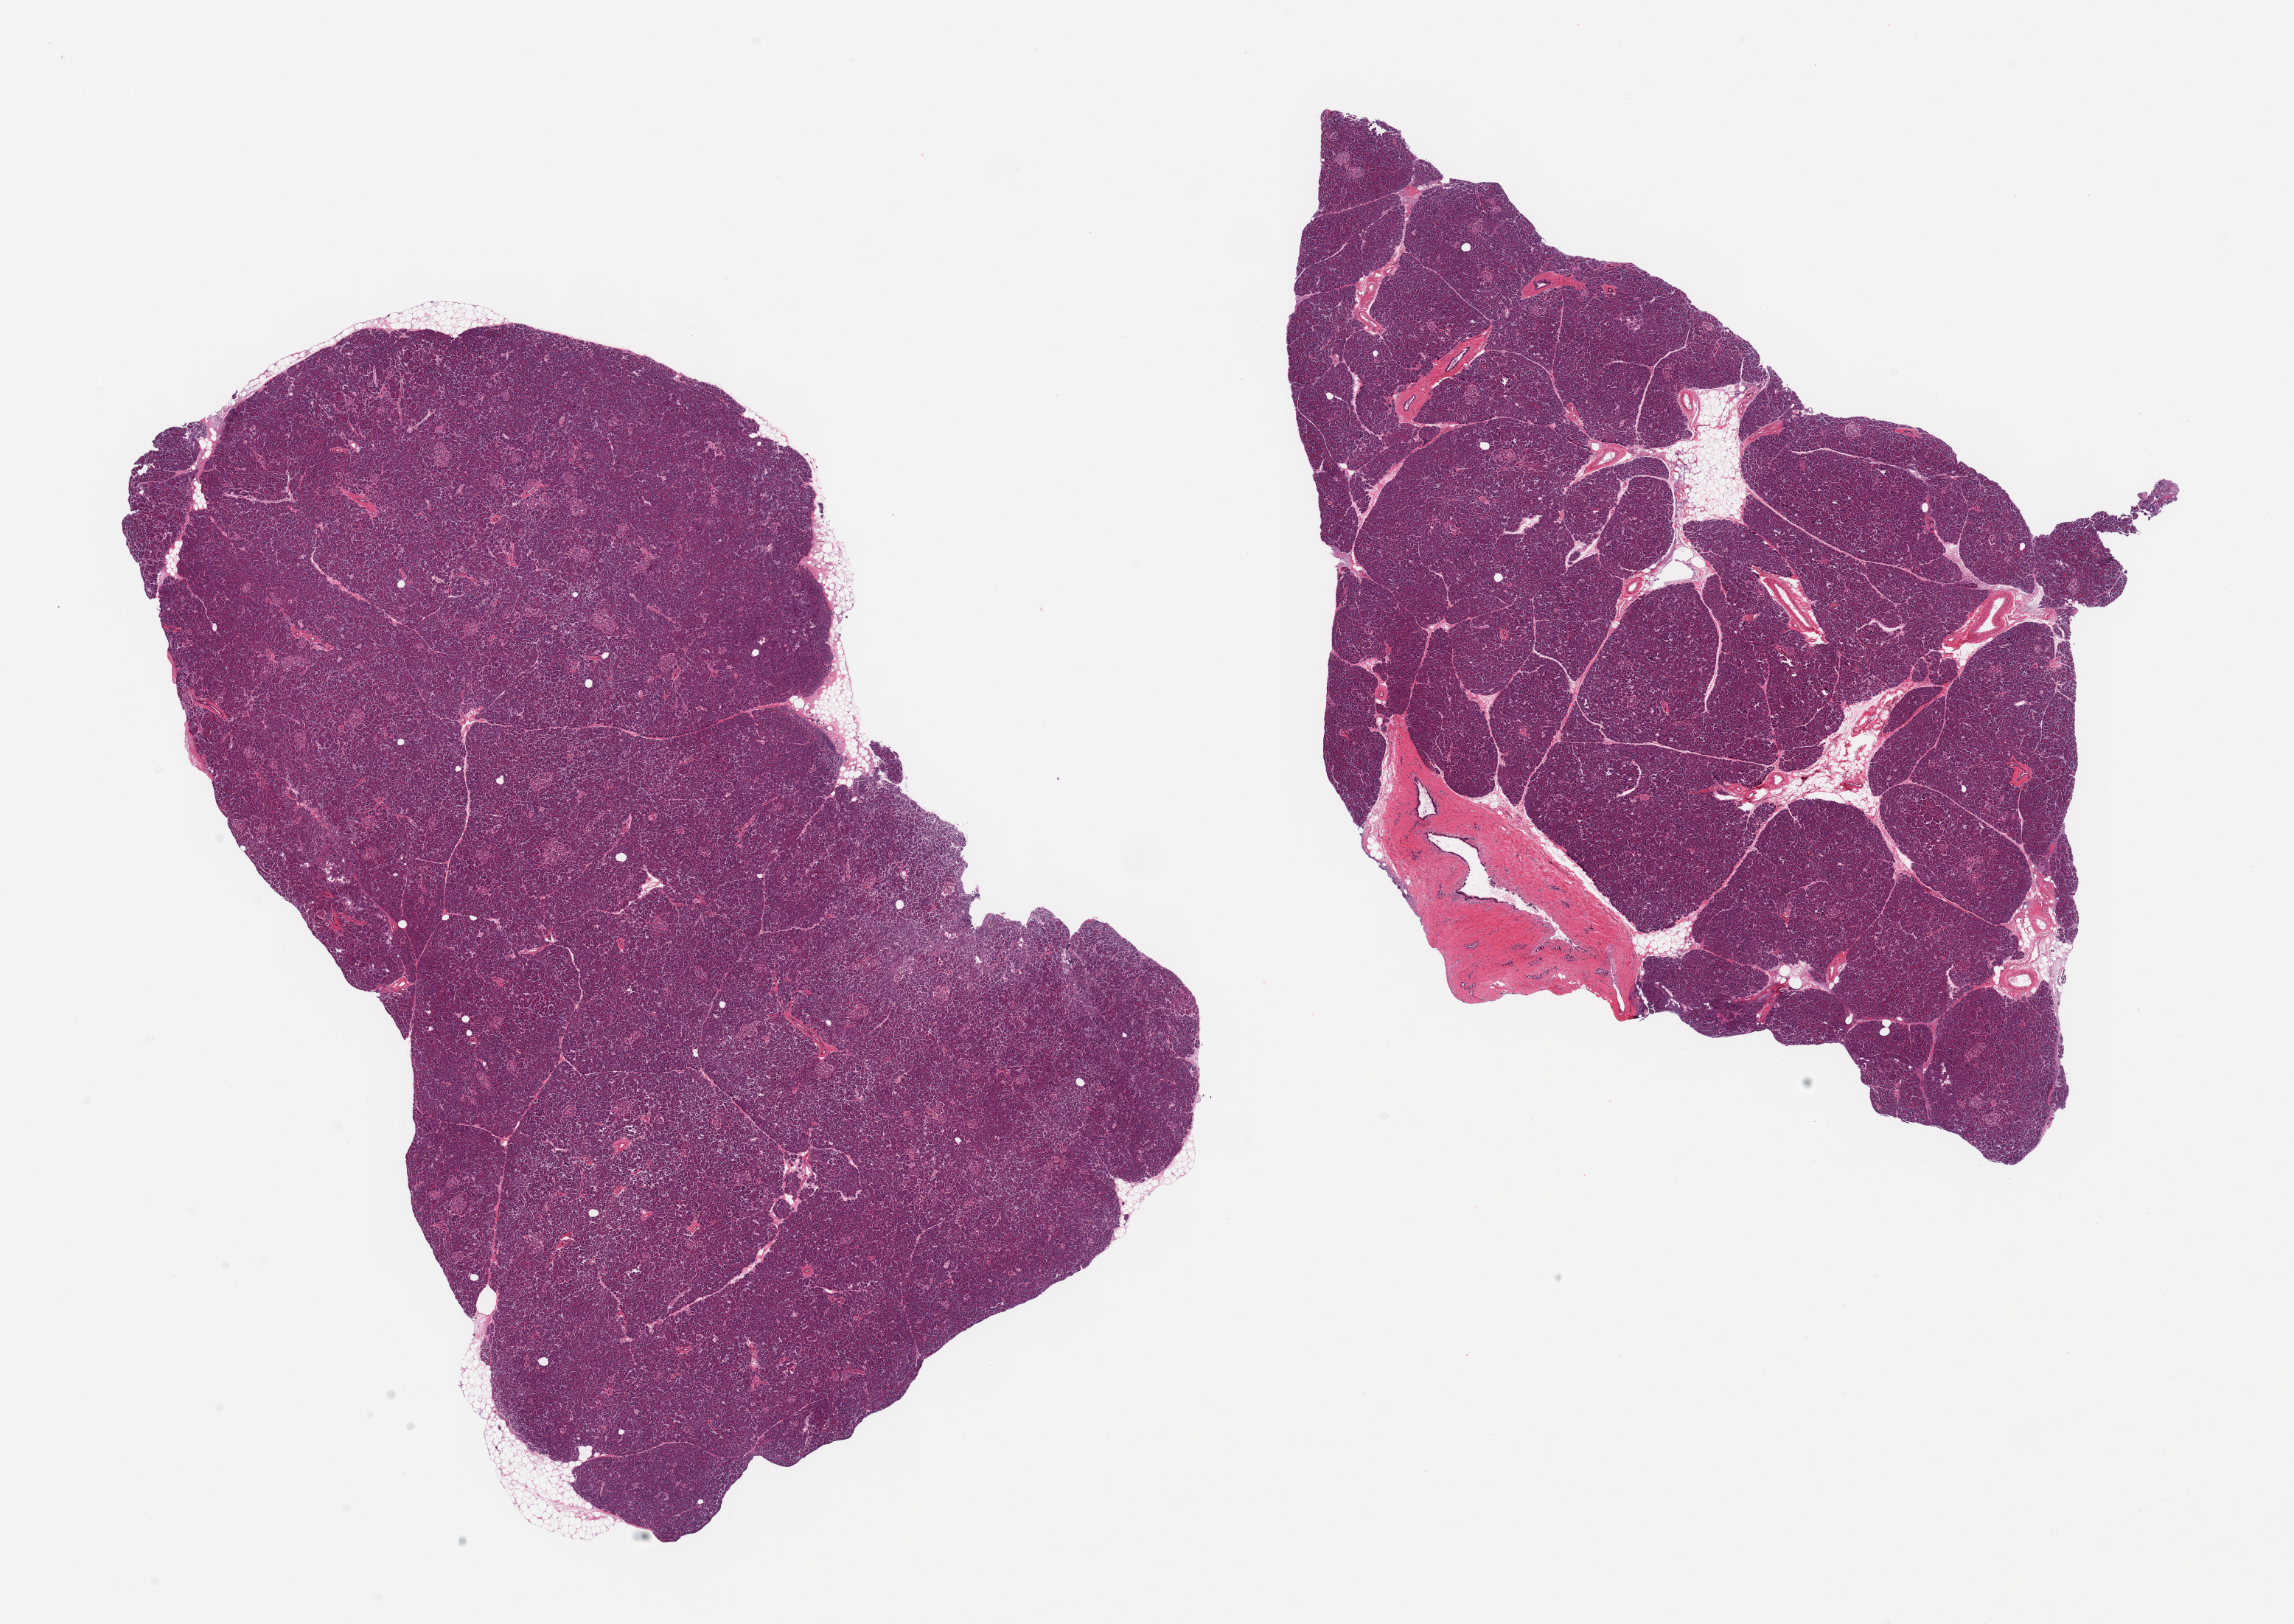
Digitized haematoxylin and eosin-stained section, a low-resolution overview of the entire scanned area, about 24.6 x 17.4 mm, PAXgene-fixed, paraffin-embedded tissue, sampled site (target tissue): pancreas, tissue donor sample.
Pathologist's review note for this sample: 2 pieces, islets numerous and well-preserved, only trace fat.